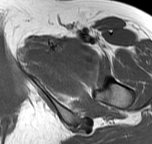
MRI of an extremity soft-tissue mass, one axial slice. Position 47 of 57 along the scan axis. MR volume resampled by the dataset authors to the PET/CT grid (not the native acquisition matrix). 3.27 mm slice thickness. 152 × 144 image matrix, field of view 148 × 141 mm. Female patient. From the clinical record (not read from this slice): histological type: pleiomorphic leiomyosarcoma; grade: intermediate; site of the primary tumour: left thigh.
Structures marked on this image (expert contour drawn on MRI and transferred to this co-registered scan by the dataset authors):
- gross tumour volume including surrounding oedema: bounding box [x1, y1, x2, y2] px = [25, 40, 89, 75]
- gross tumour volume (mass): [61, 44, 83, 61]